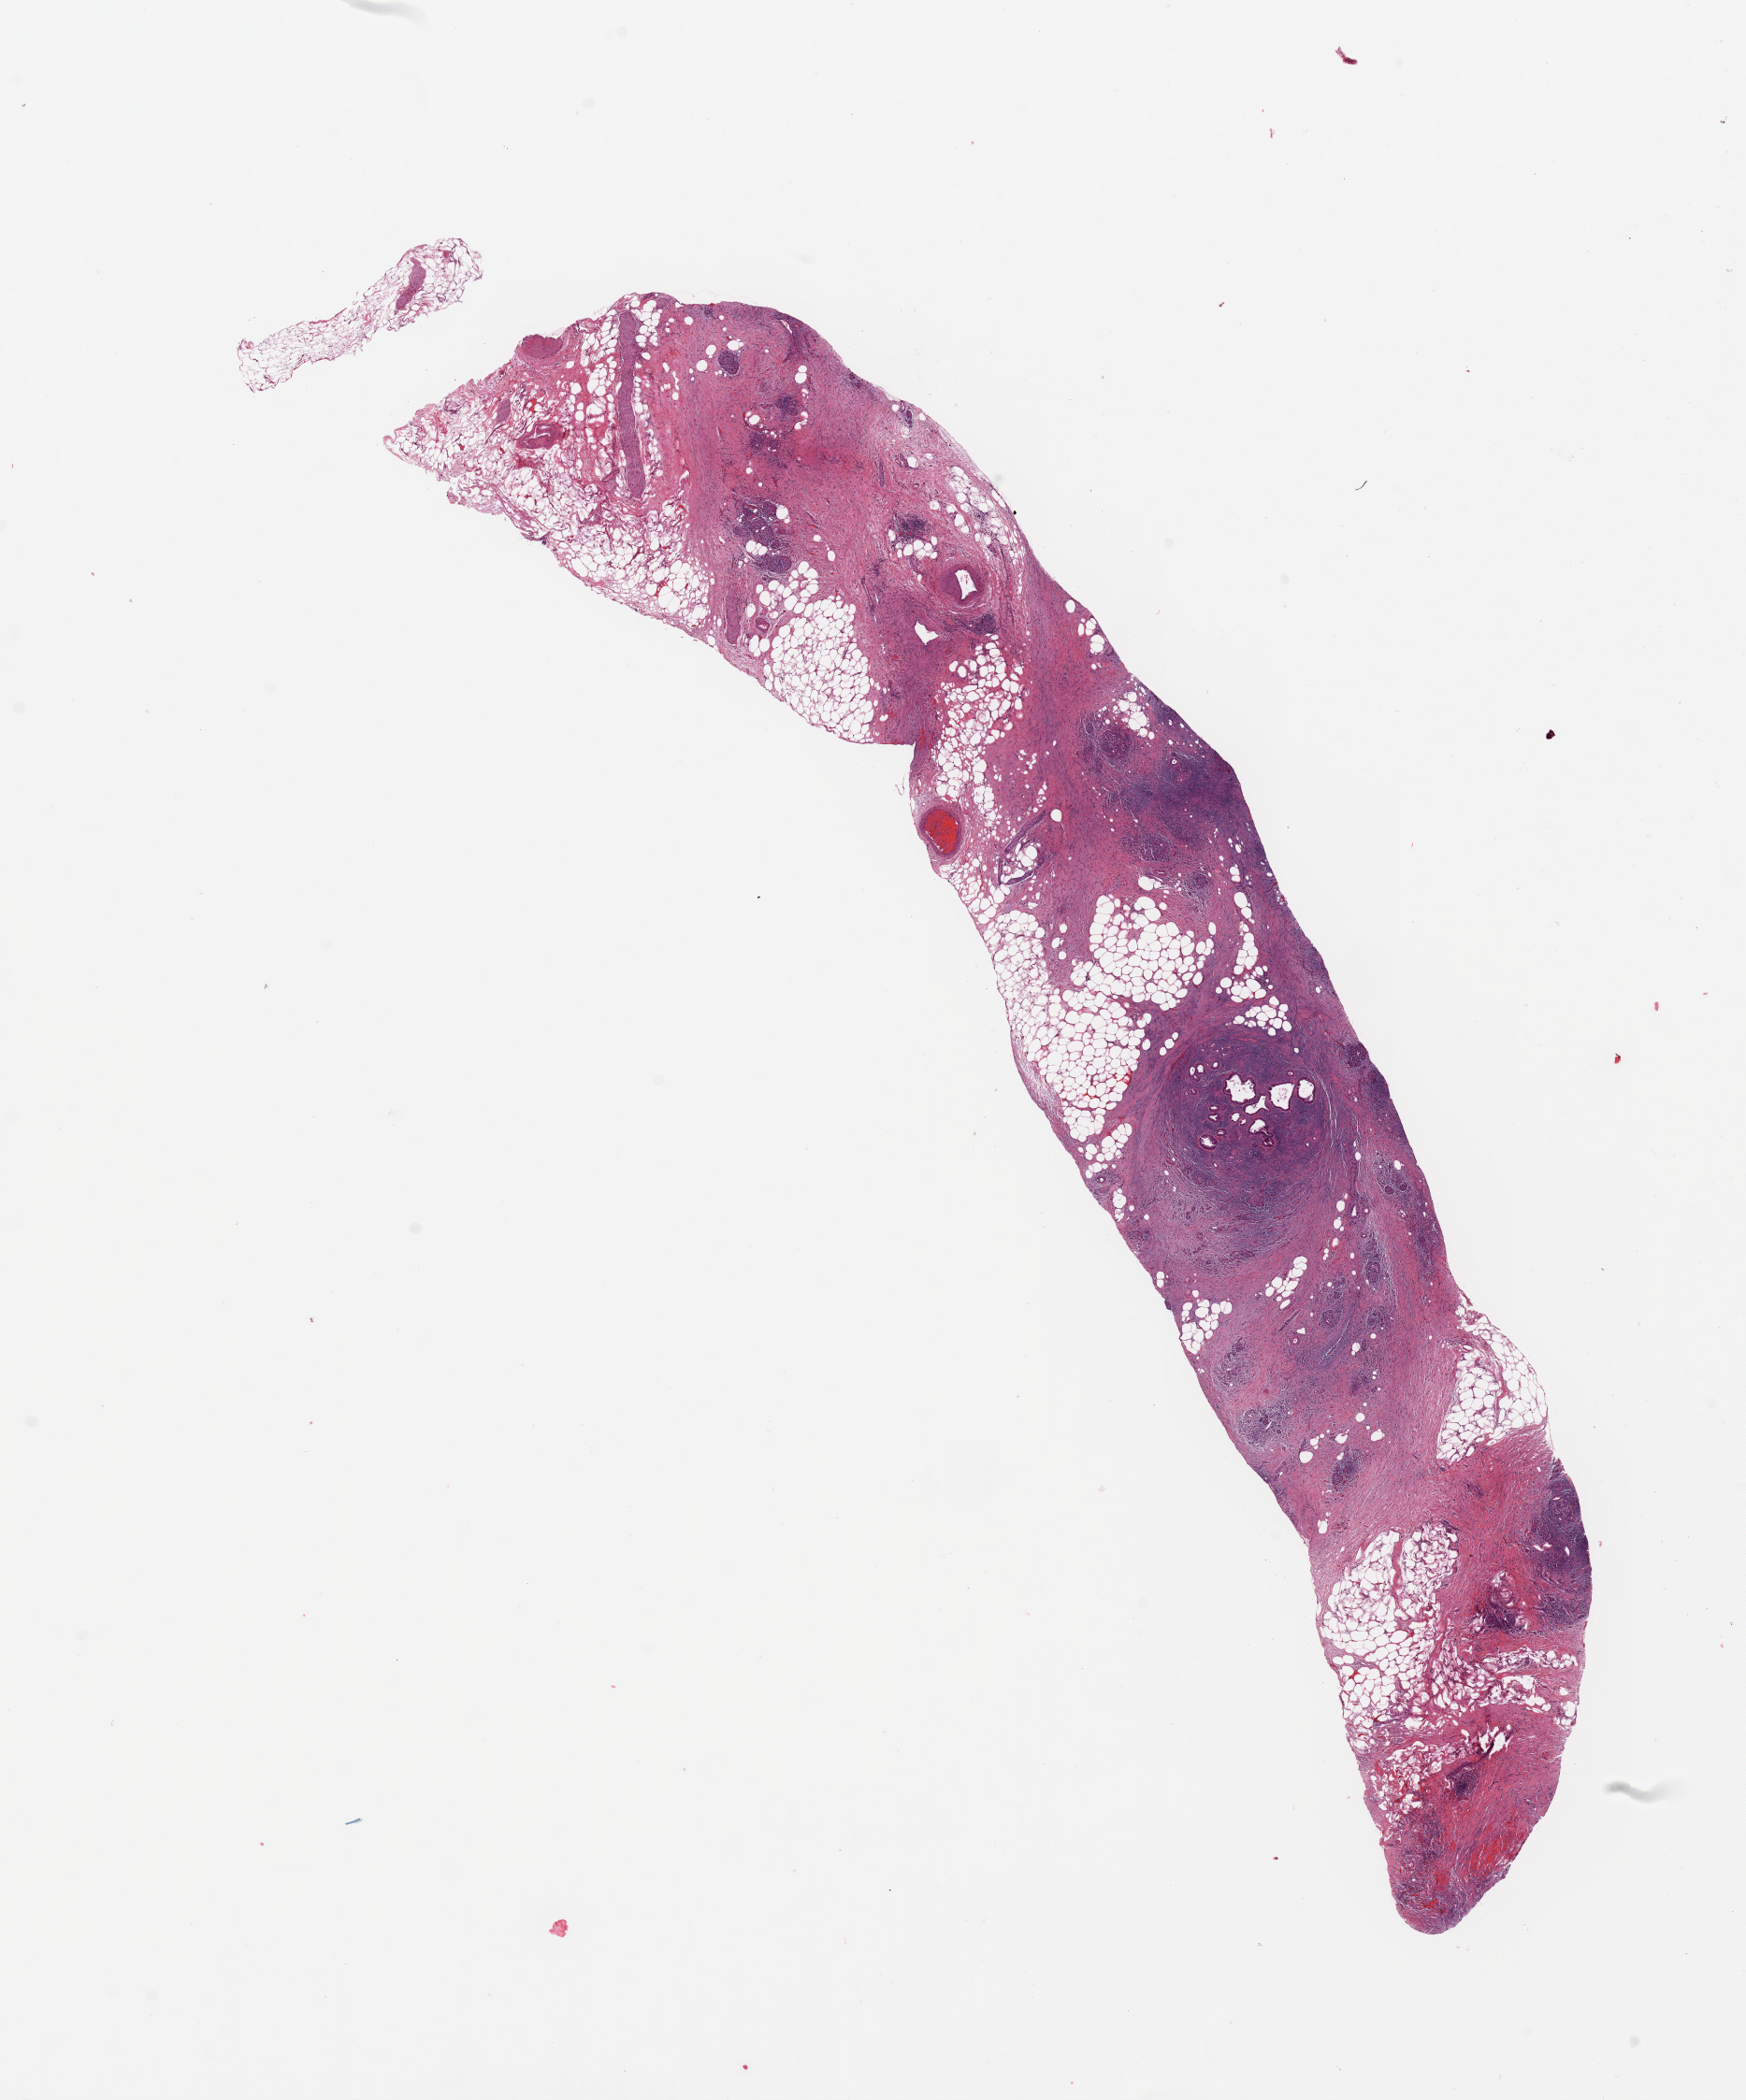
Whole-slide histology image, H&E, whole scanned area (about 14.8 x 17.8 mm, acquisition: 20x scan) shown as a low-resolution overview. Pancreas, tissue type not recorded.
Patient diagnosis (cohort enrolment): ductal adenocarcinoma (pancreas).